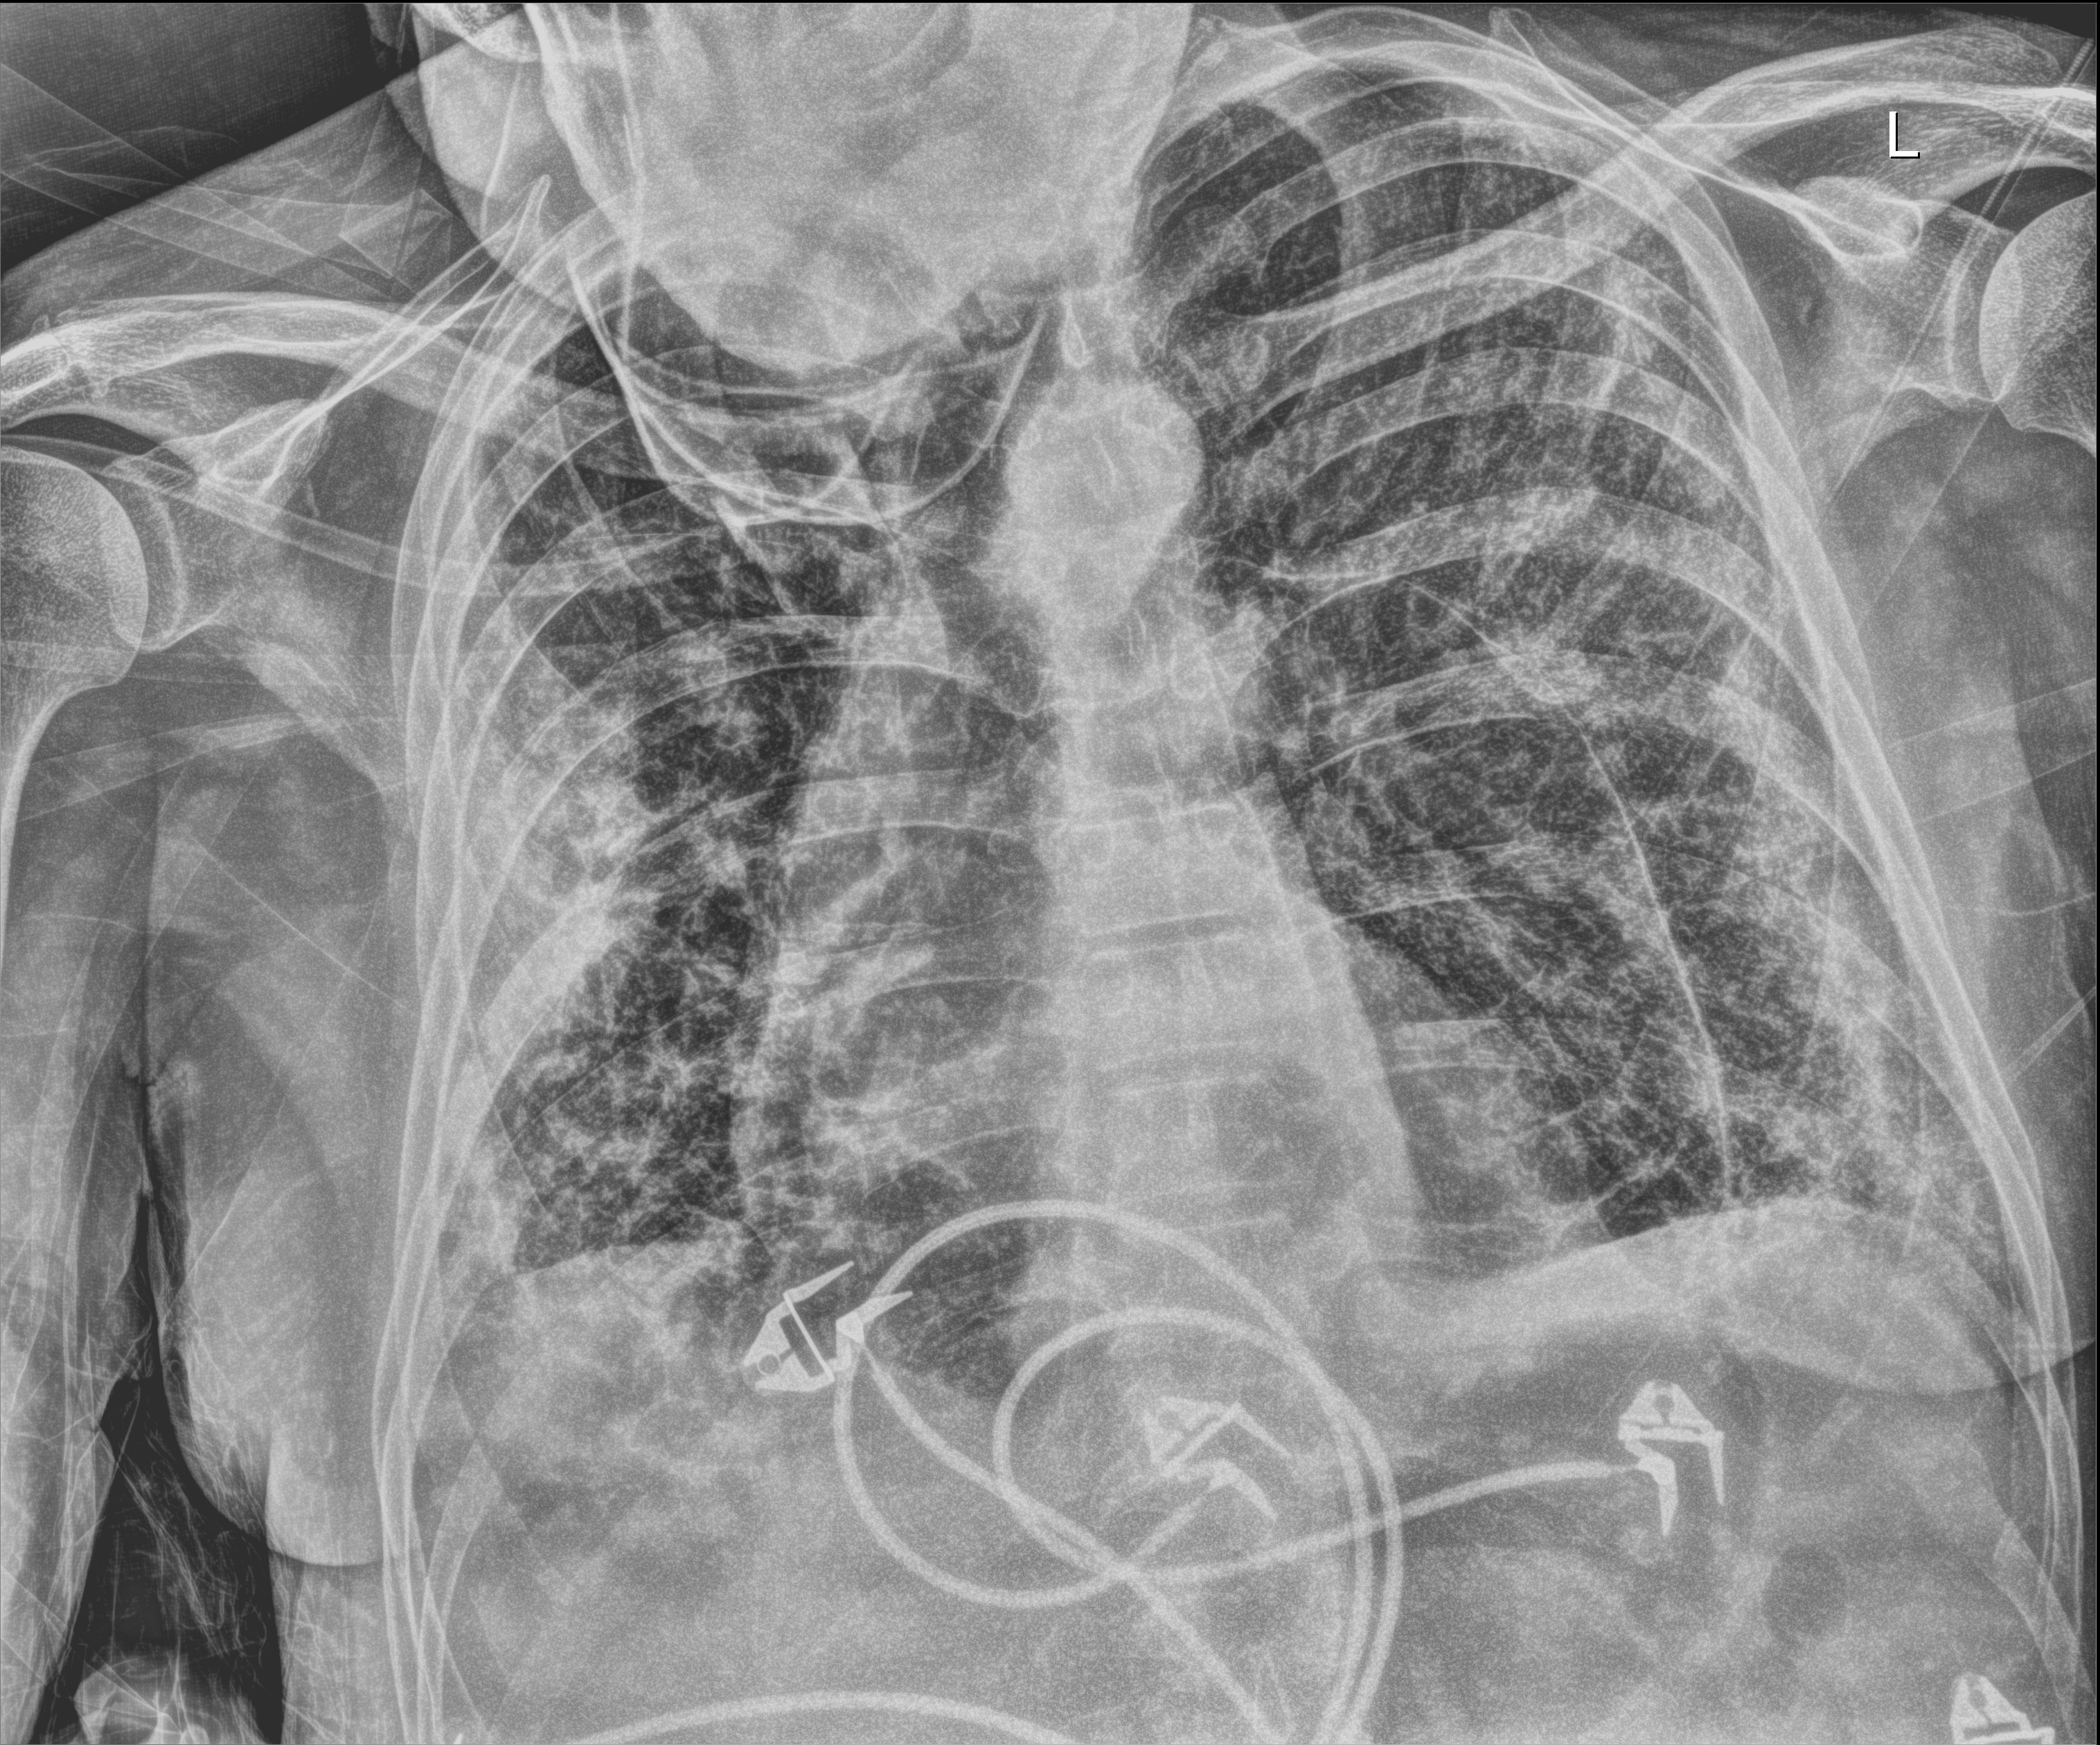
Bedside chest radiograph (digital radiography); anteroposterior (AP) projection. Male patient hospitalised with COVID-19, age 60–74 years.
From the hospital-stay record, not from the radiograph (when in the stay this image was taken is not recorded): admitted to intensive care during this hospital stay: no; mechanically ventilated during this hospital stay: no.